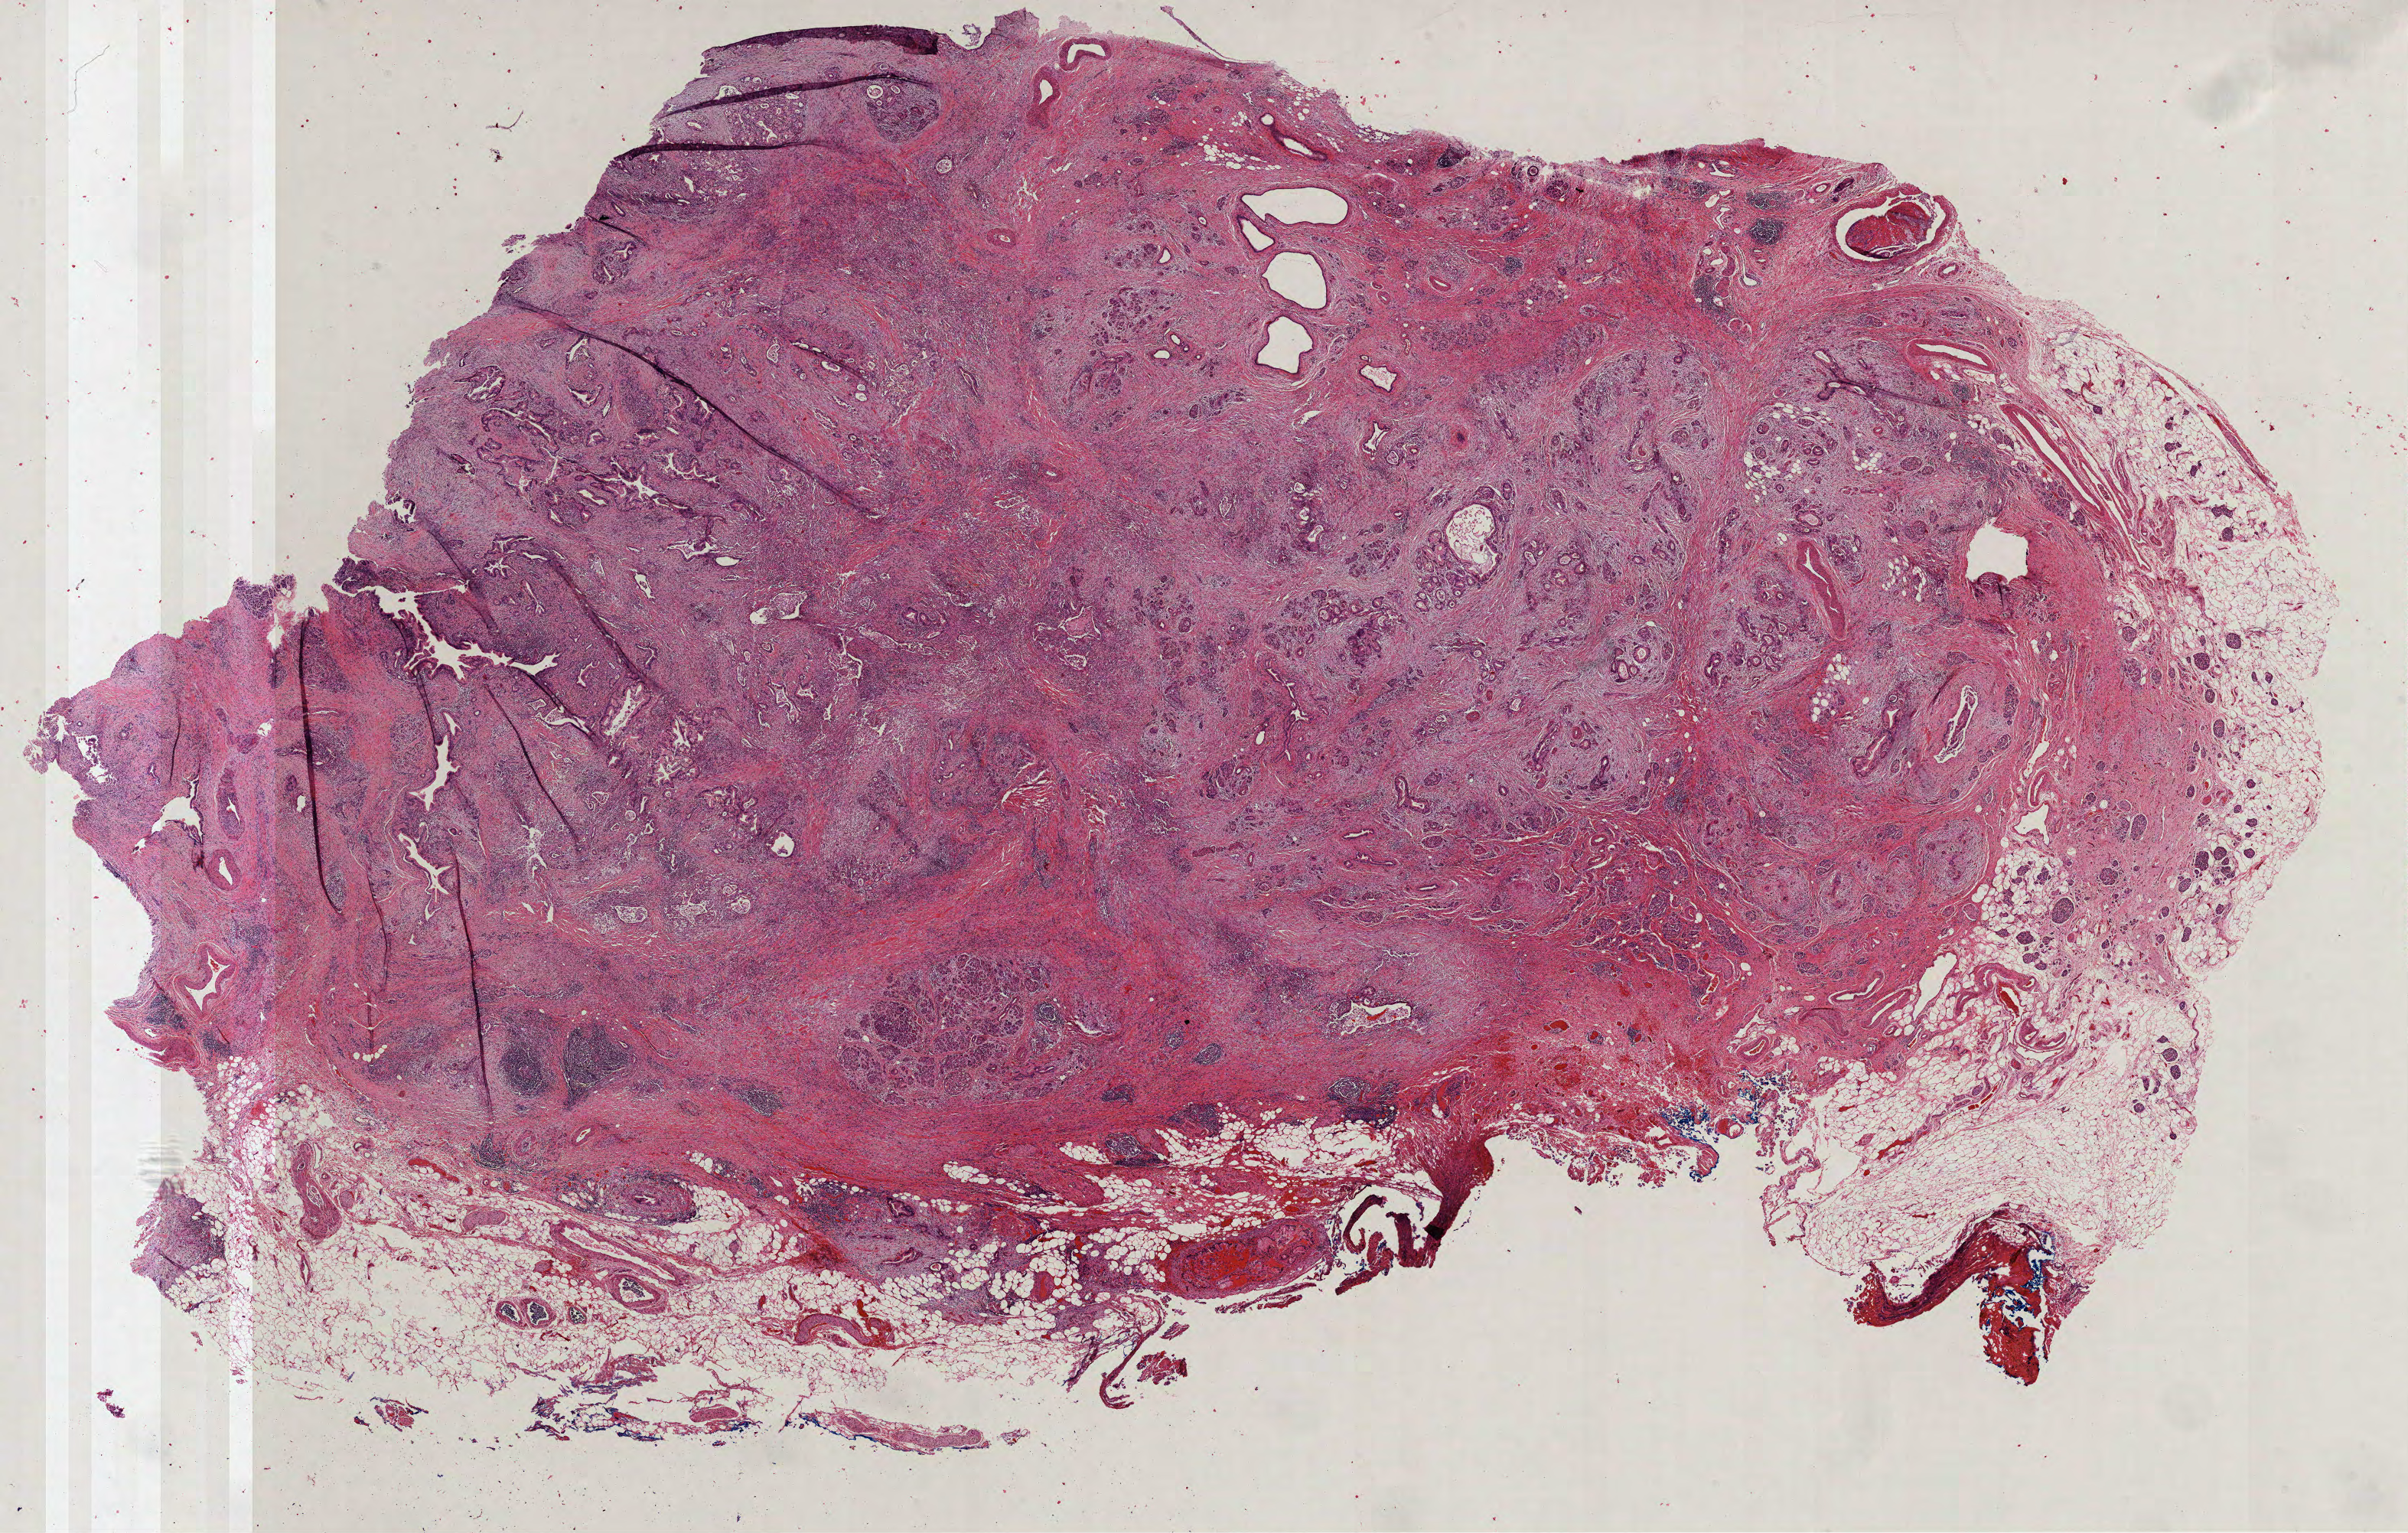
Whole-slide histology image, H&E-stained — shown as a low-resolution overview of the whole scanned area (about 25.4 x 16.2 mm), formalin-fixed paraffin-embedded (FFPE) diagnostic section, primary tumour sample from the pancreas. Patient: female, age at initial diagnosis 59 years. Histologic grade: G3 (poorly differentiated).
Pathologic diagnosis: Infiltrating duct carcinoma, NOS (head of pancreas). Lymph nodes positive (case pathology): 9 of 11 examined. AJCC pathologic stage: IIB (6th edition).